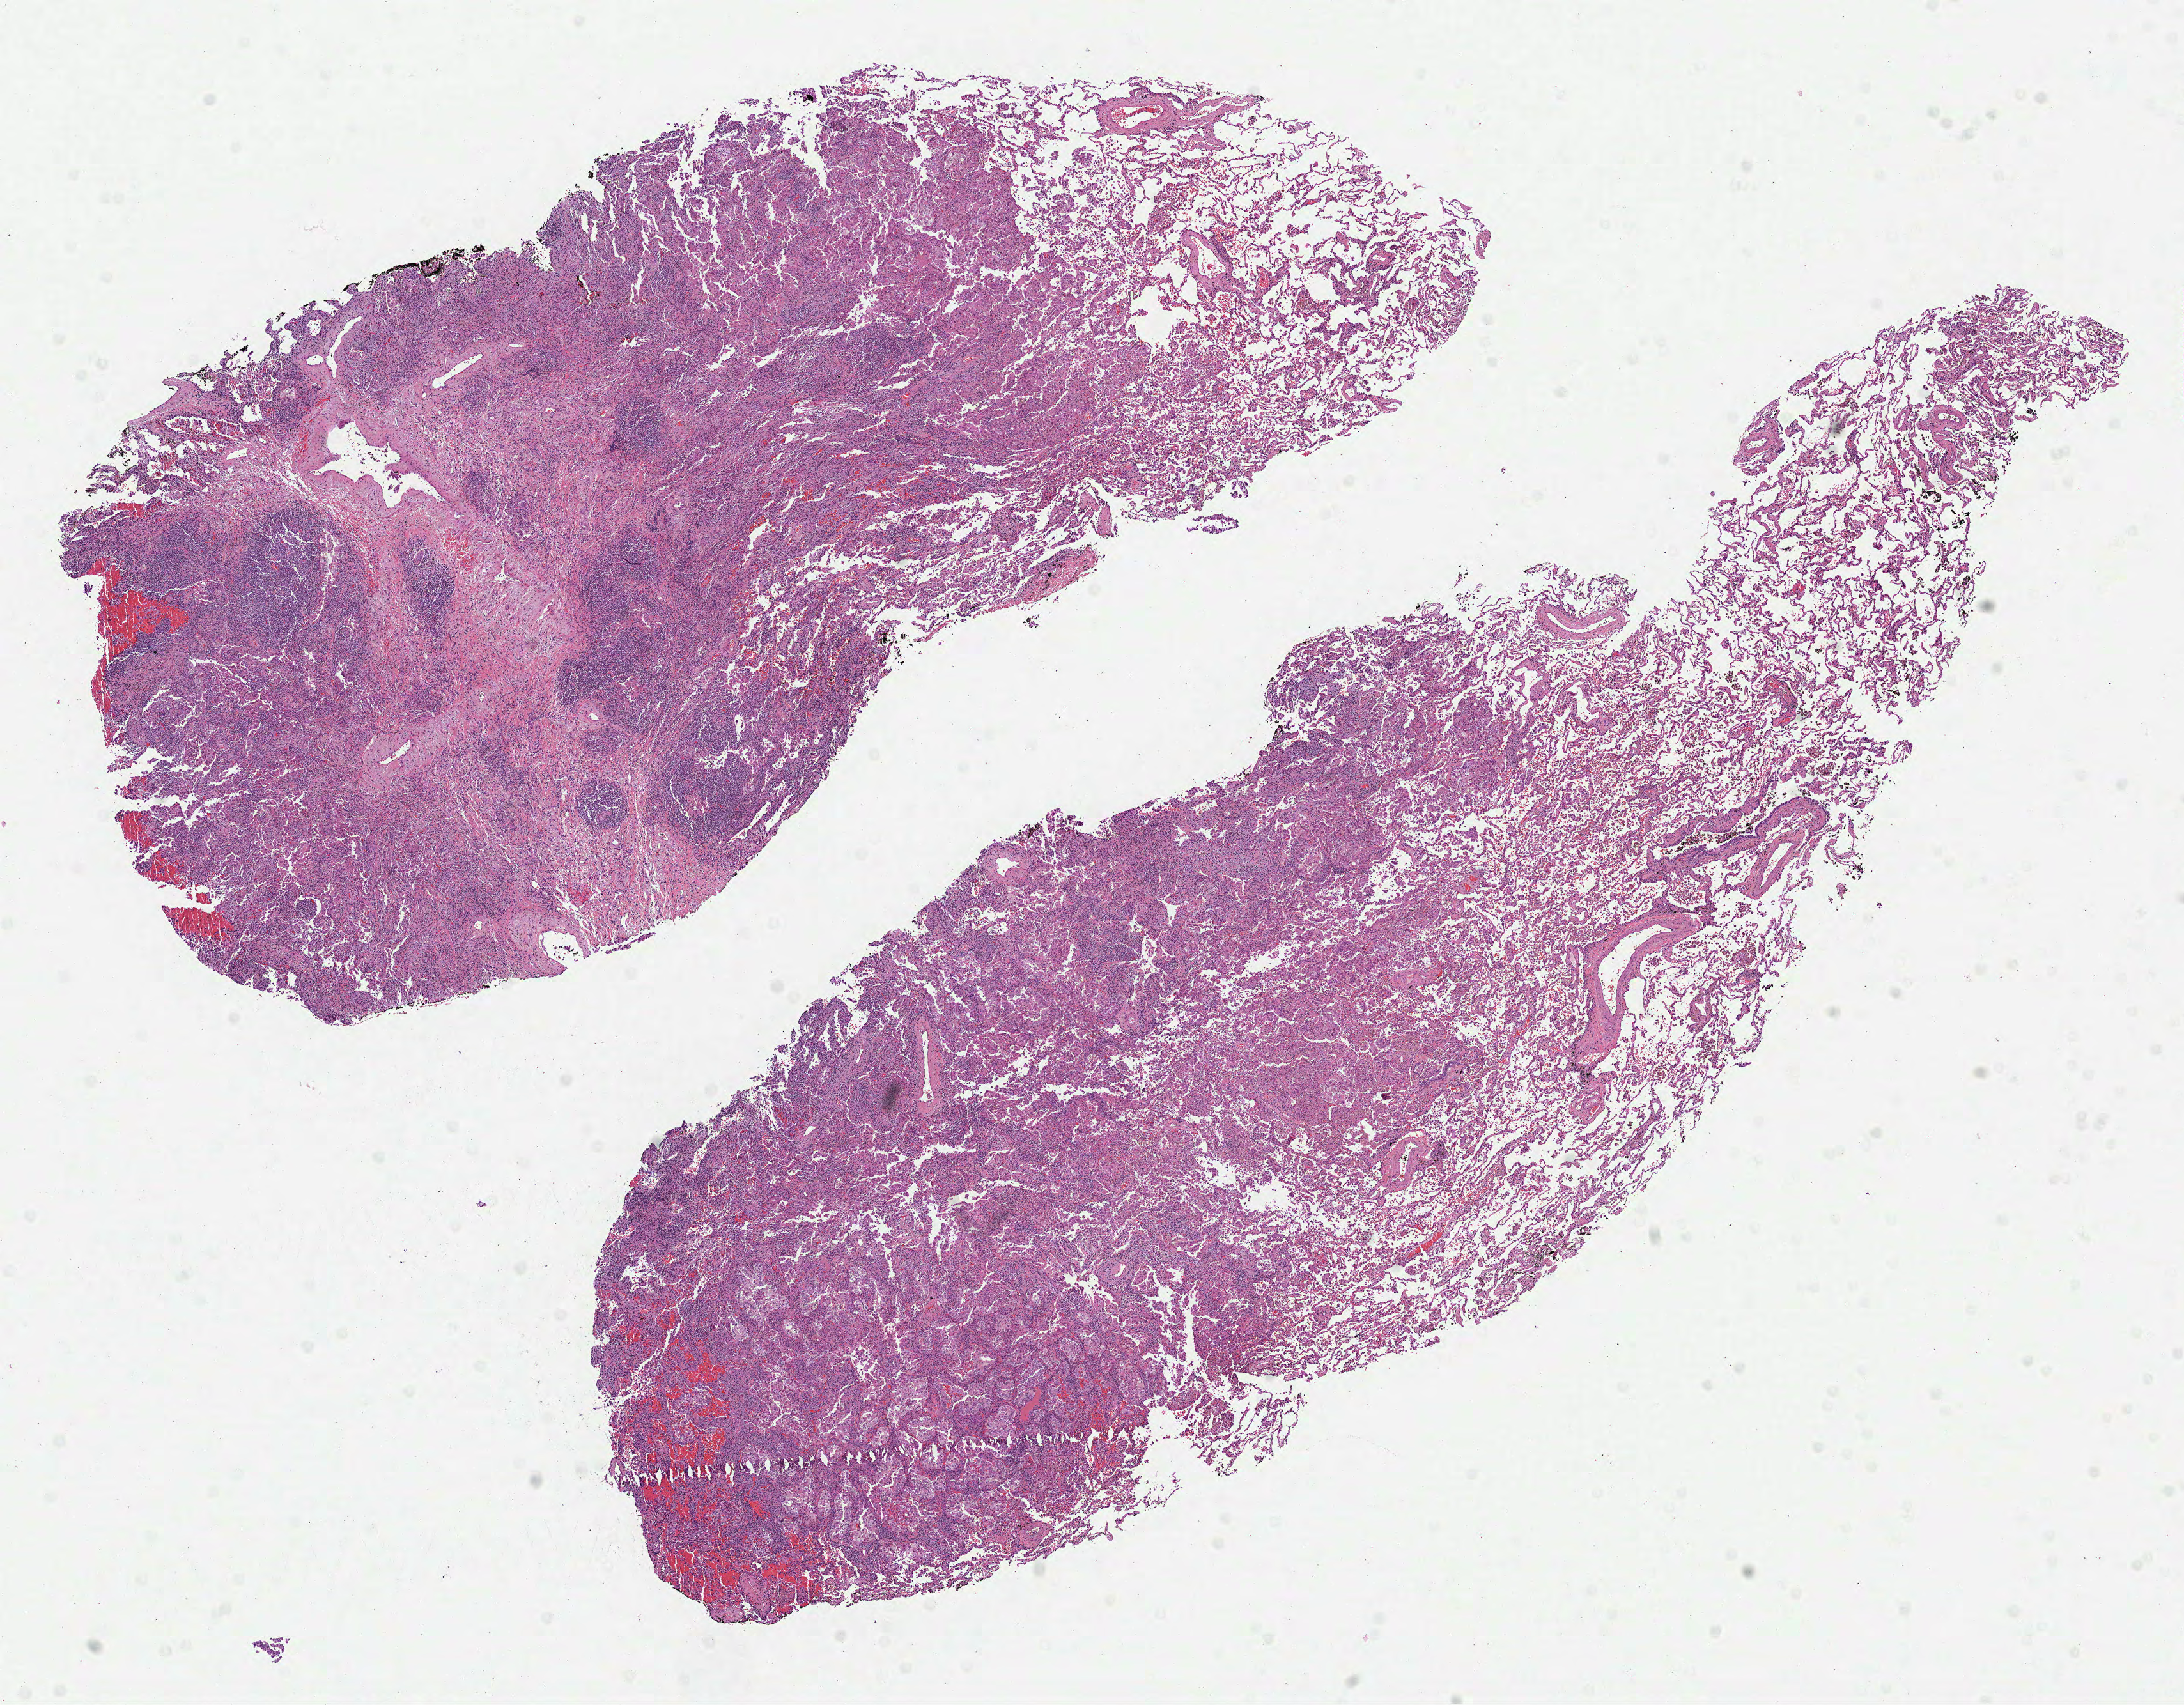
H&E-stained whole-slide image — shown as a low-resolution overview of the whole scanned area (about 13.8 x 10.8 mm); formalin-fixed paraffin-embedded (FFPE) diagnostic section; primary tumour sample from the lung. Female patient; age at initial diagnosis 70 years.
Laterality: right. Histologic diagnosis: Adenocarcinoma, NOS (middle lobe, lung). AJCC pathologic stage: IA (7th edition).